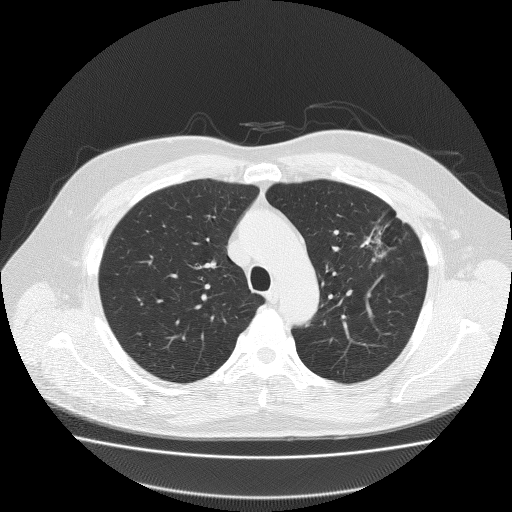
Low-dose screening chest CT, axial slice, baseline annual screen, lung window (W 1500 / L -600 HU), lung (sharp) reconstruction kernel (FC51). Male participant, aged 62 years at enrolment. Former smoker at enrolment.
Expert reader's lesion annotation, bounding box [x1, y1, x2, y2] px = [355, 202, 423, 261]. Reader record for this screening exam (exam-level; its link to the box is not recorded): non-calcified nodule or mass ≥4 mm, left upper lobe, 18 × 8 mm, spiculated (stellate) margins, soft tissue attenuation. Participant outcome: lung cancer diagnosed 49 days after this screen — bronchiolo-alveolar adenocarcinoma, NOS, left upper lobe, well differentiated (G1), stage IA (AJCC 6th edition), 25 mm at pathology.